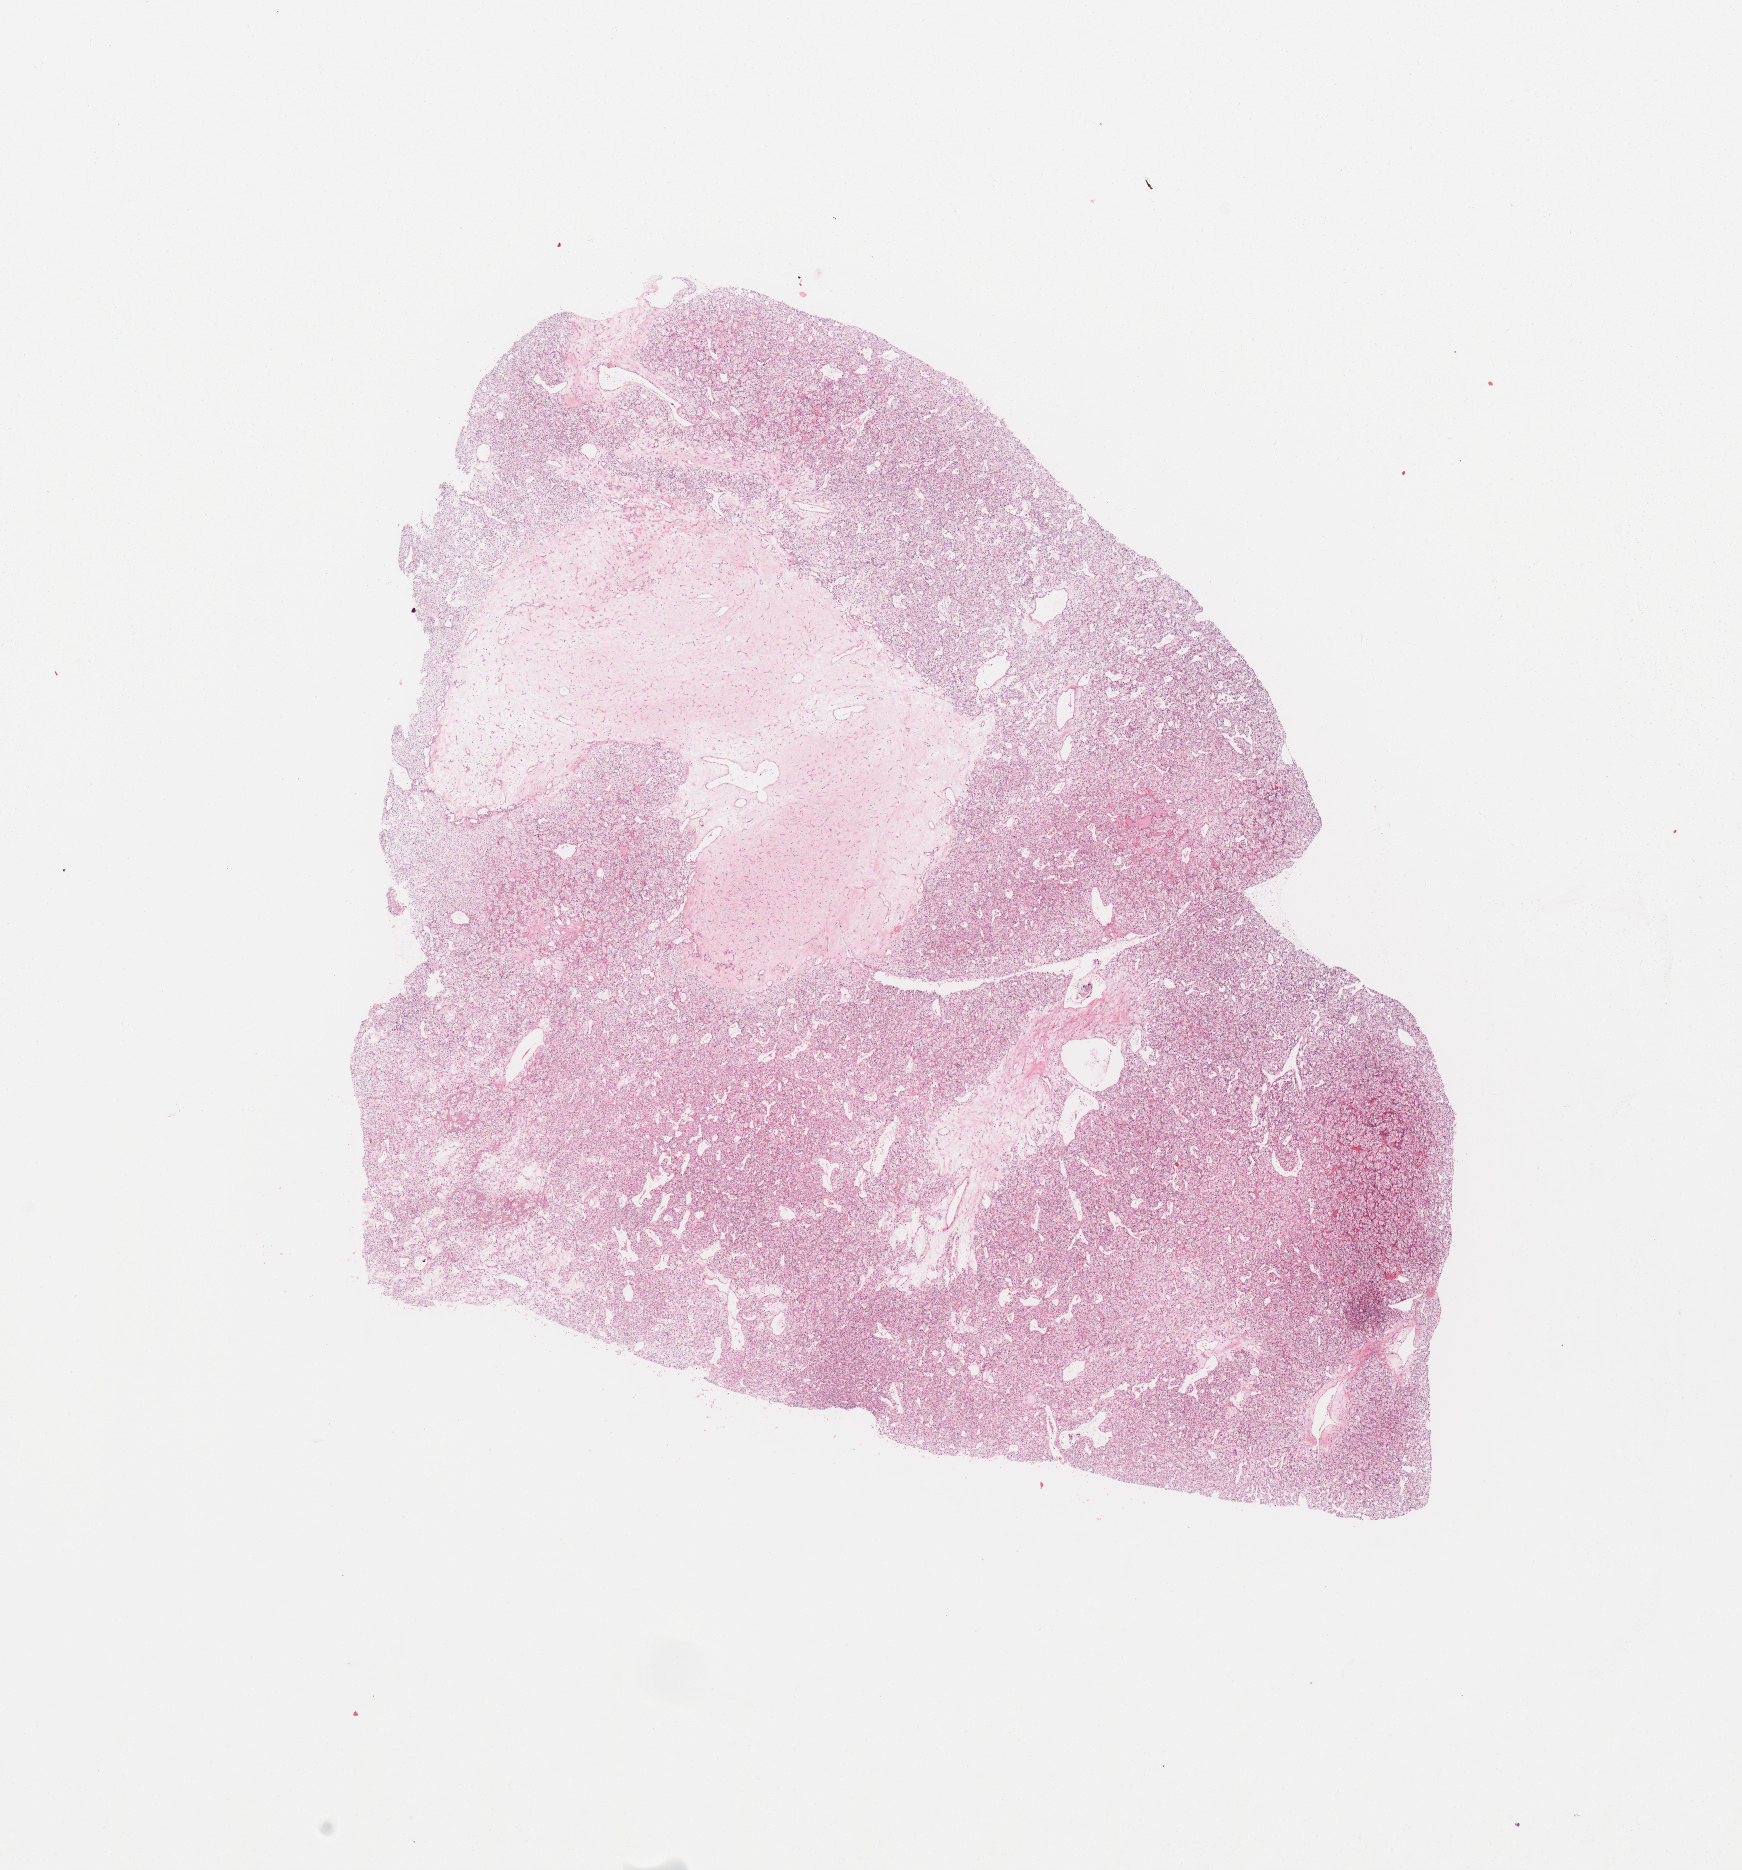
Digitized H&E tissue section (whole slide) — a low-resolution overview of the entire scanned area, about 13.8 x 14.8 mm (slide scanned at 20x), tumour tissue sample, sampled site: kidney. Male, 47 y/o. Histologic grade: G2 (moderately differentiated). Slide review estimates, as recorded: tumour nuclei 80%, necrosis 0%.
• AJCC pathologic stage: IV
• diagnosis: Renal cell carcinoma, NOS